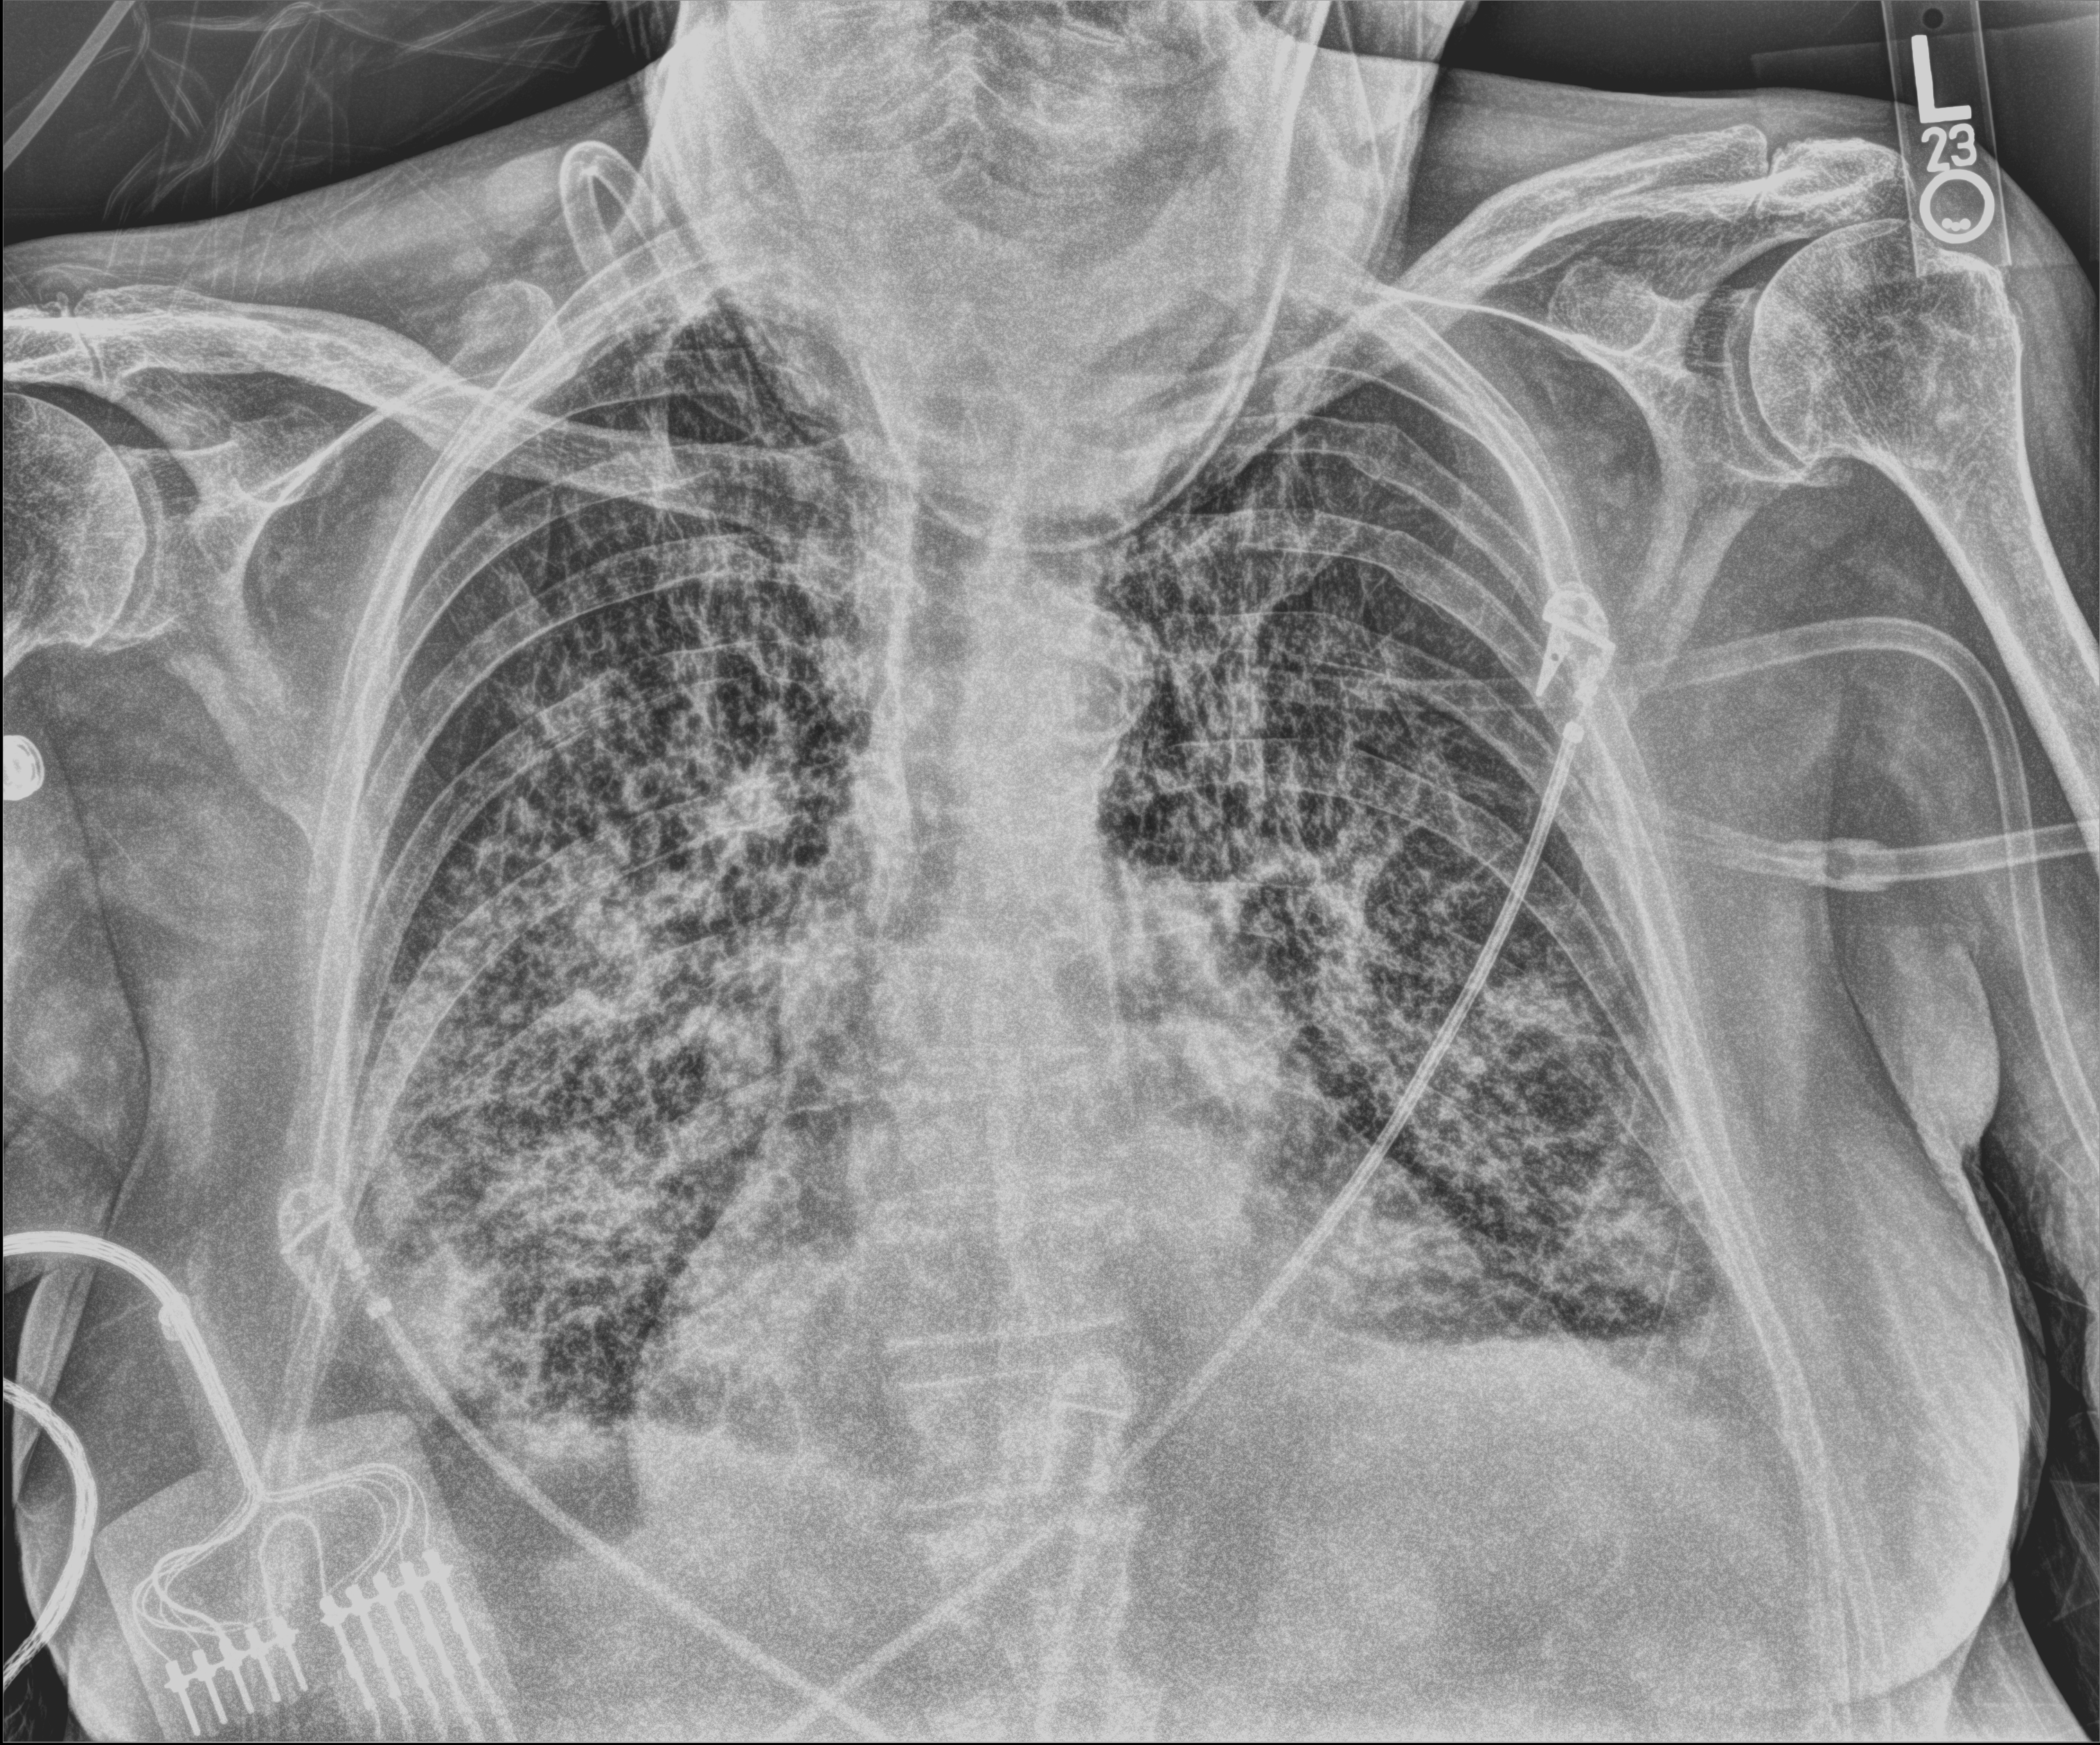
Portable chest radiograph, anteroposterior (AP) projection. Male patient hospitalised with COVID-19, age 75–90 years.
Hospital-stay facts (about this admission, not read from this image; timing relative to this image not recorded): chronic kidney disease (admission record): no; smoking status (admission record): former.